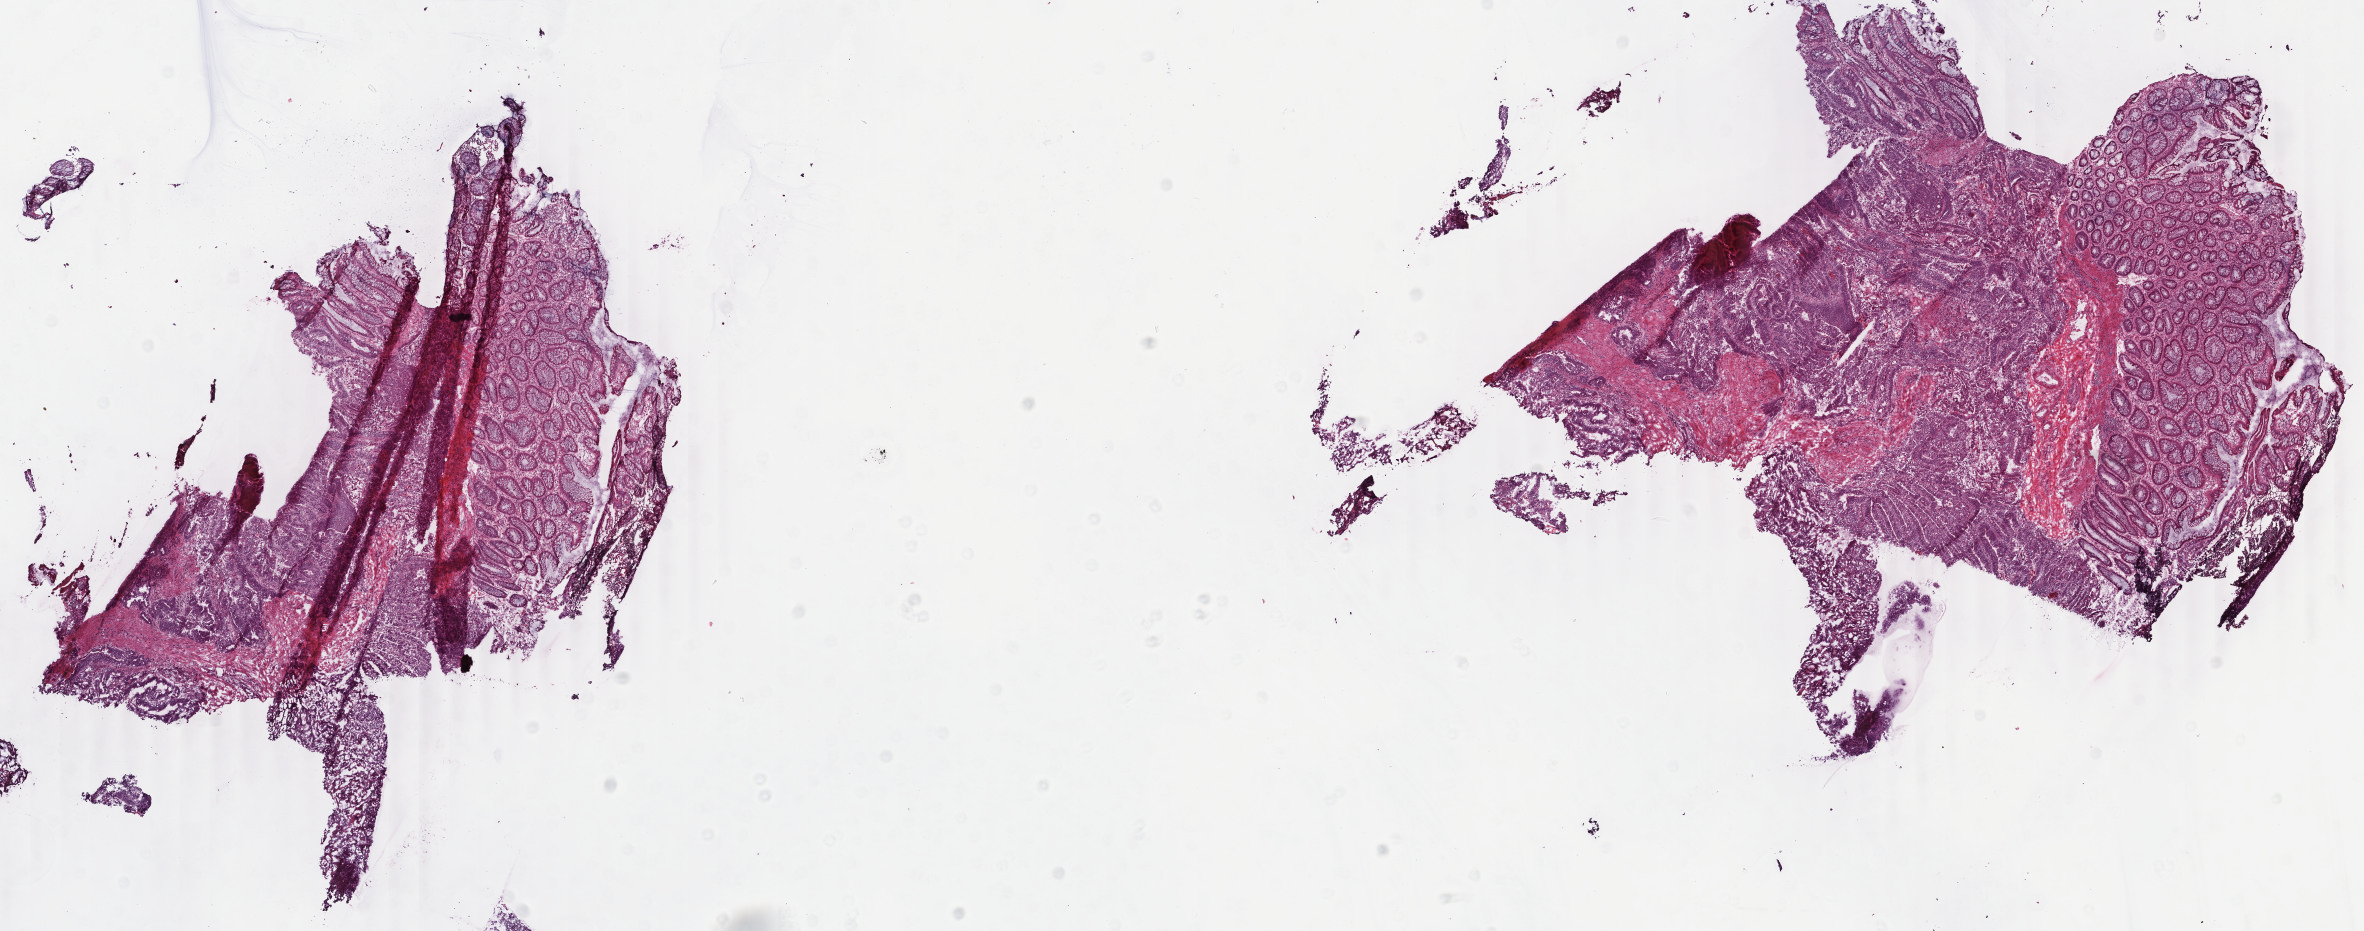
Digitized H&E tissue section (whole slide), shown as a low-resolution overview of the whole scanned area (about 18.8 x 7.4 mm, acquisition: 40x scan); frozen section; colon, primary tumour sample. Female, age 80 years at initial diagnosis. Pathologist review of this section (percent, as recorded): tumour cells 55%, tumour nuclei 65%, normal cells 35%, stromal cells 9%, necrosis 1%. Inflammatory infiltration, as recorded: lymphocyte infiltration 12%, monocyte infiltration 6%, neutrophil infiltration 1%.
Lymph nodes positive (case pathology): 2 of 14 examined. Pathologic diagnosis: Adenocarcinoma, NOS (sigmoid colon). AJCC pathologic stage: III (5th edition).